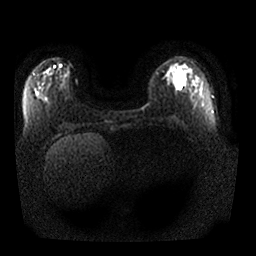
Breast MRI, one axial slice. Diffusion-weighted series; image 2 of 4 stored at this slice position (different b-values; order by instance number). 1.5 T. 4 mm slice thickness. 256 × 256 image matrix, field of view 350 × 350 mm. Female patient.
Annotated regions visible in this slice (manually delineated by an expert):
- tumour on diffusion-weighted imaging: bounding box (x1, y1, x2, y2) in pixels: (171, 67, 180, 80)